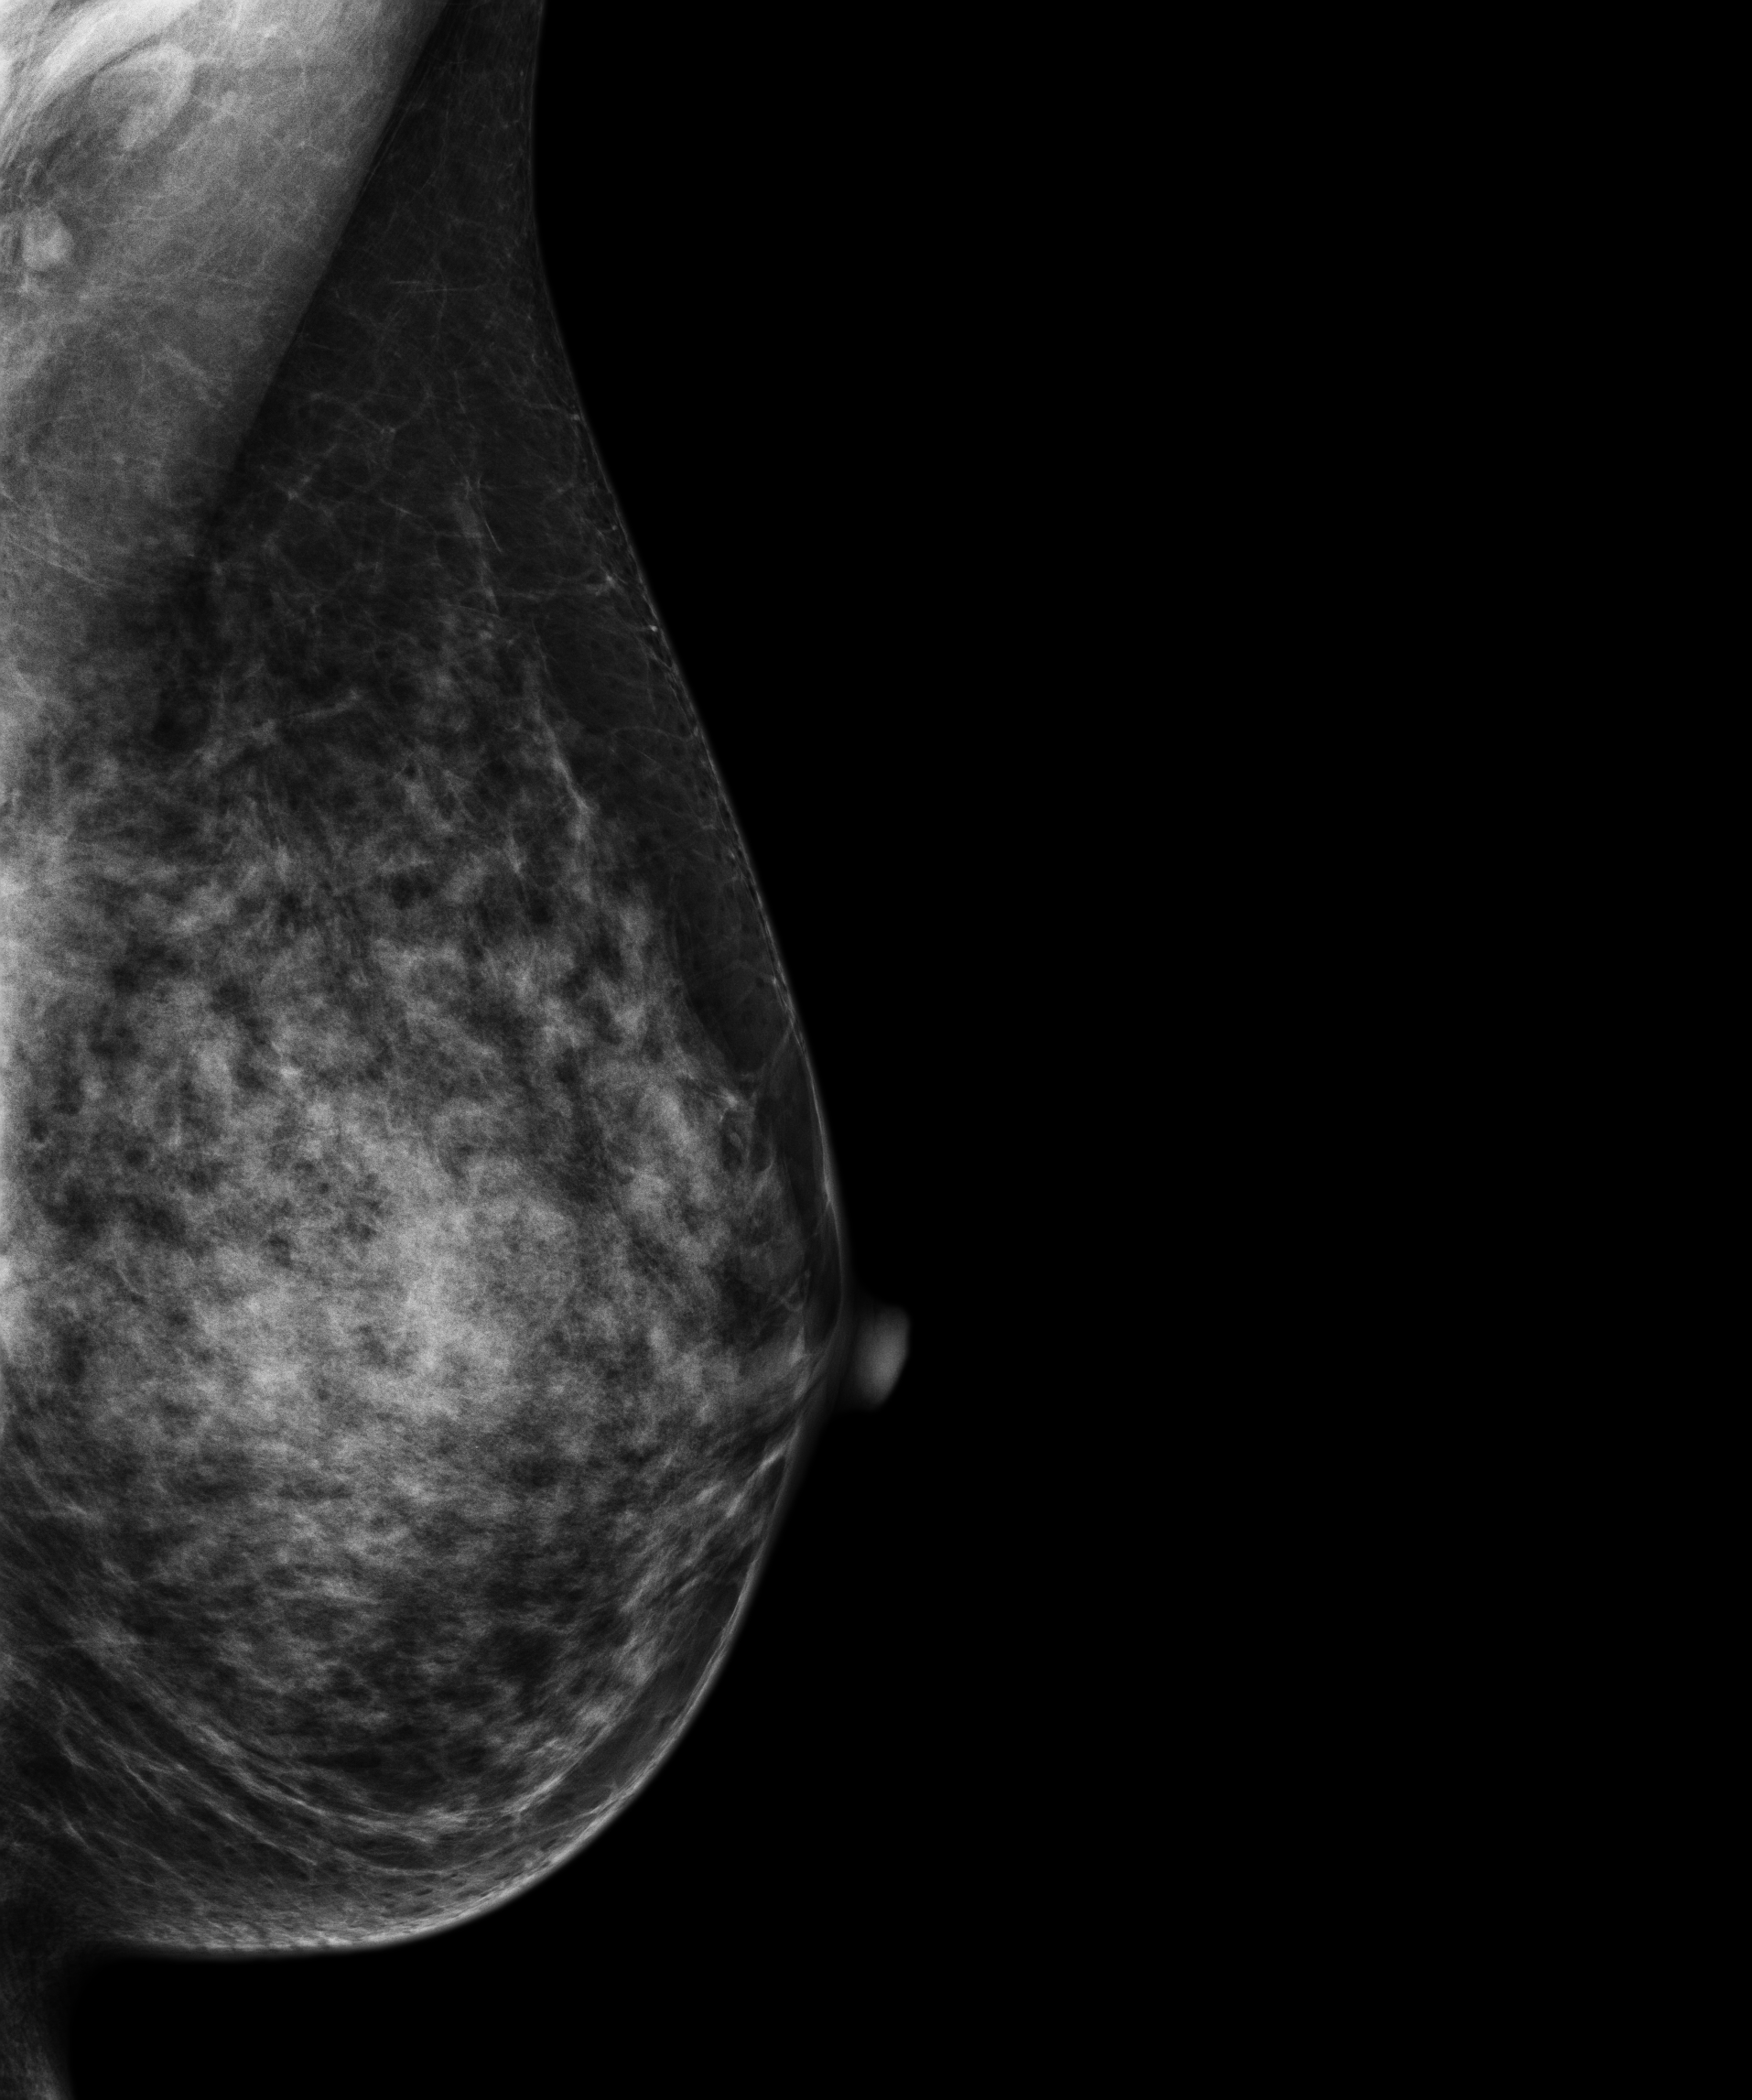
Digital mammogram (FFDM); left breast; MLO view; annual screening mammography examination; compressed breast thickness 46 mm; system: Senographe Essential ADS_56.21.3. Patient aged 60 years (female).
Breast density at the screening exam (both breasts): extremely dense (BI-RADS density category d). Final BI-RADS assessment for this screening round (tomosynthesis exam, both breasts): category 1. Recall: no recall after this screen.